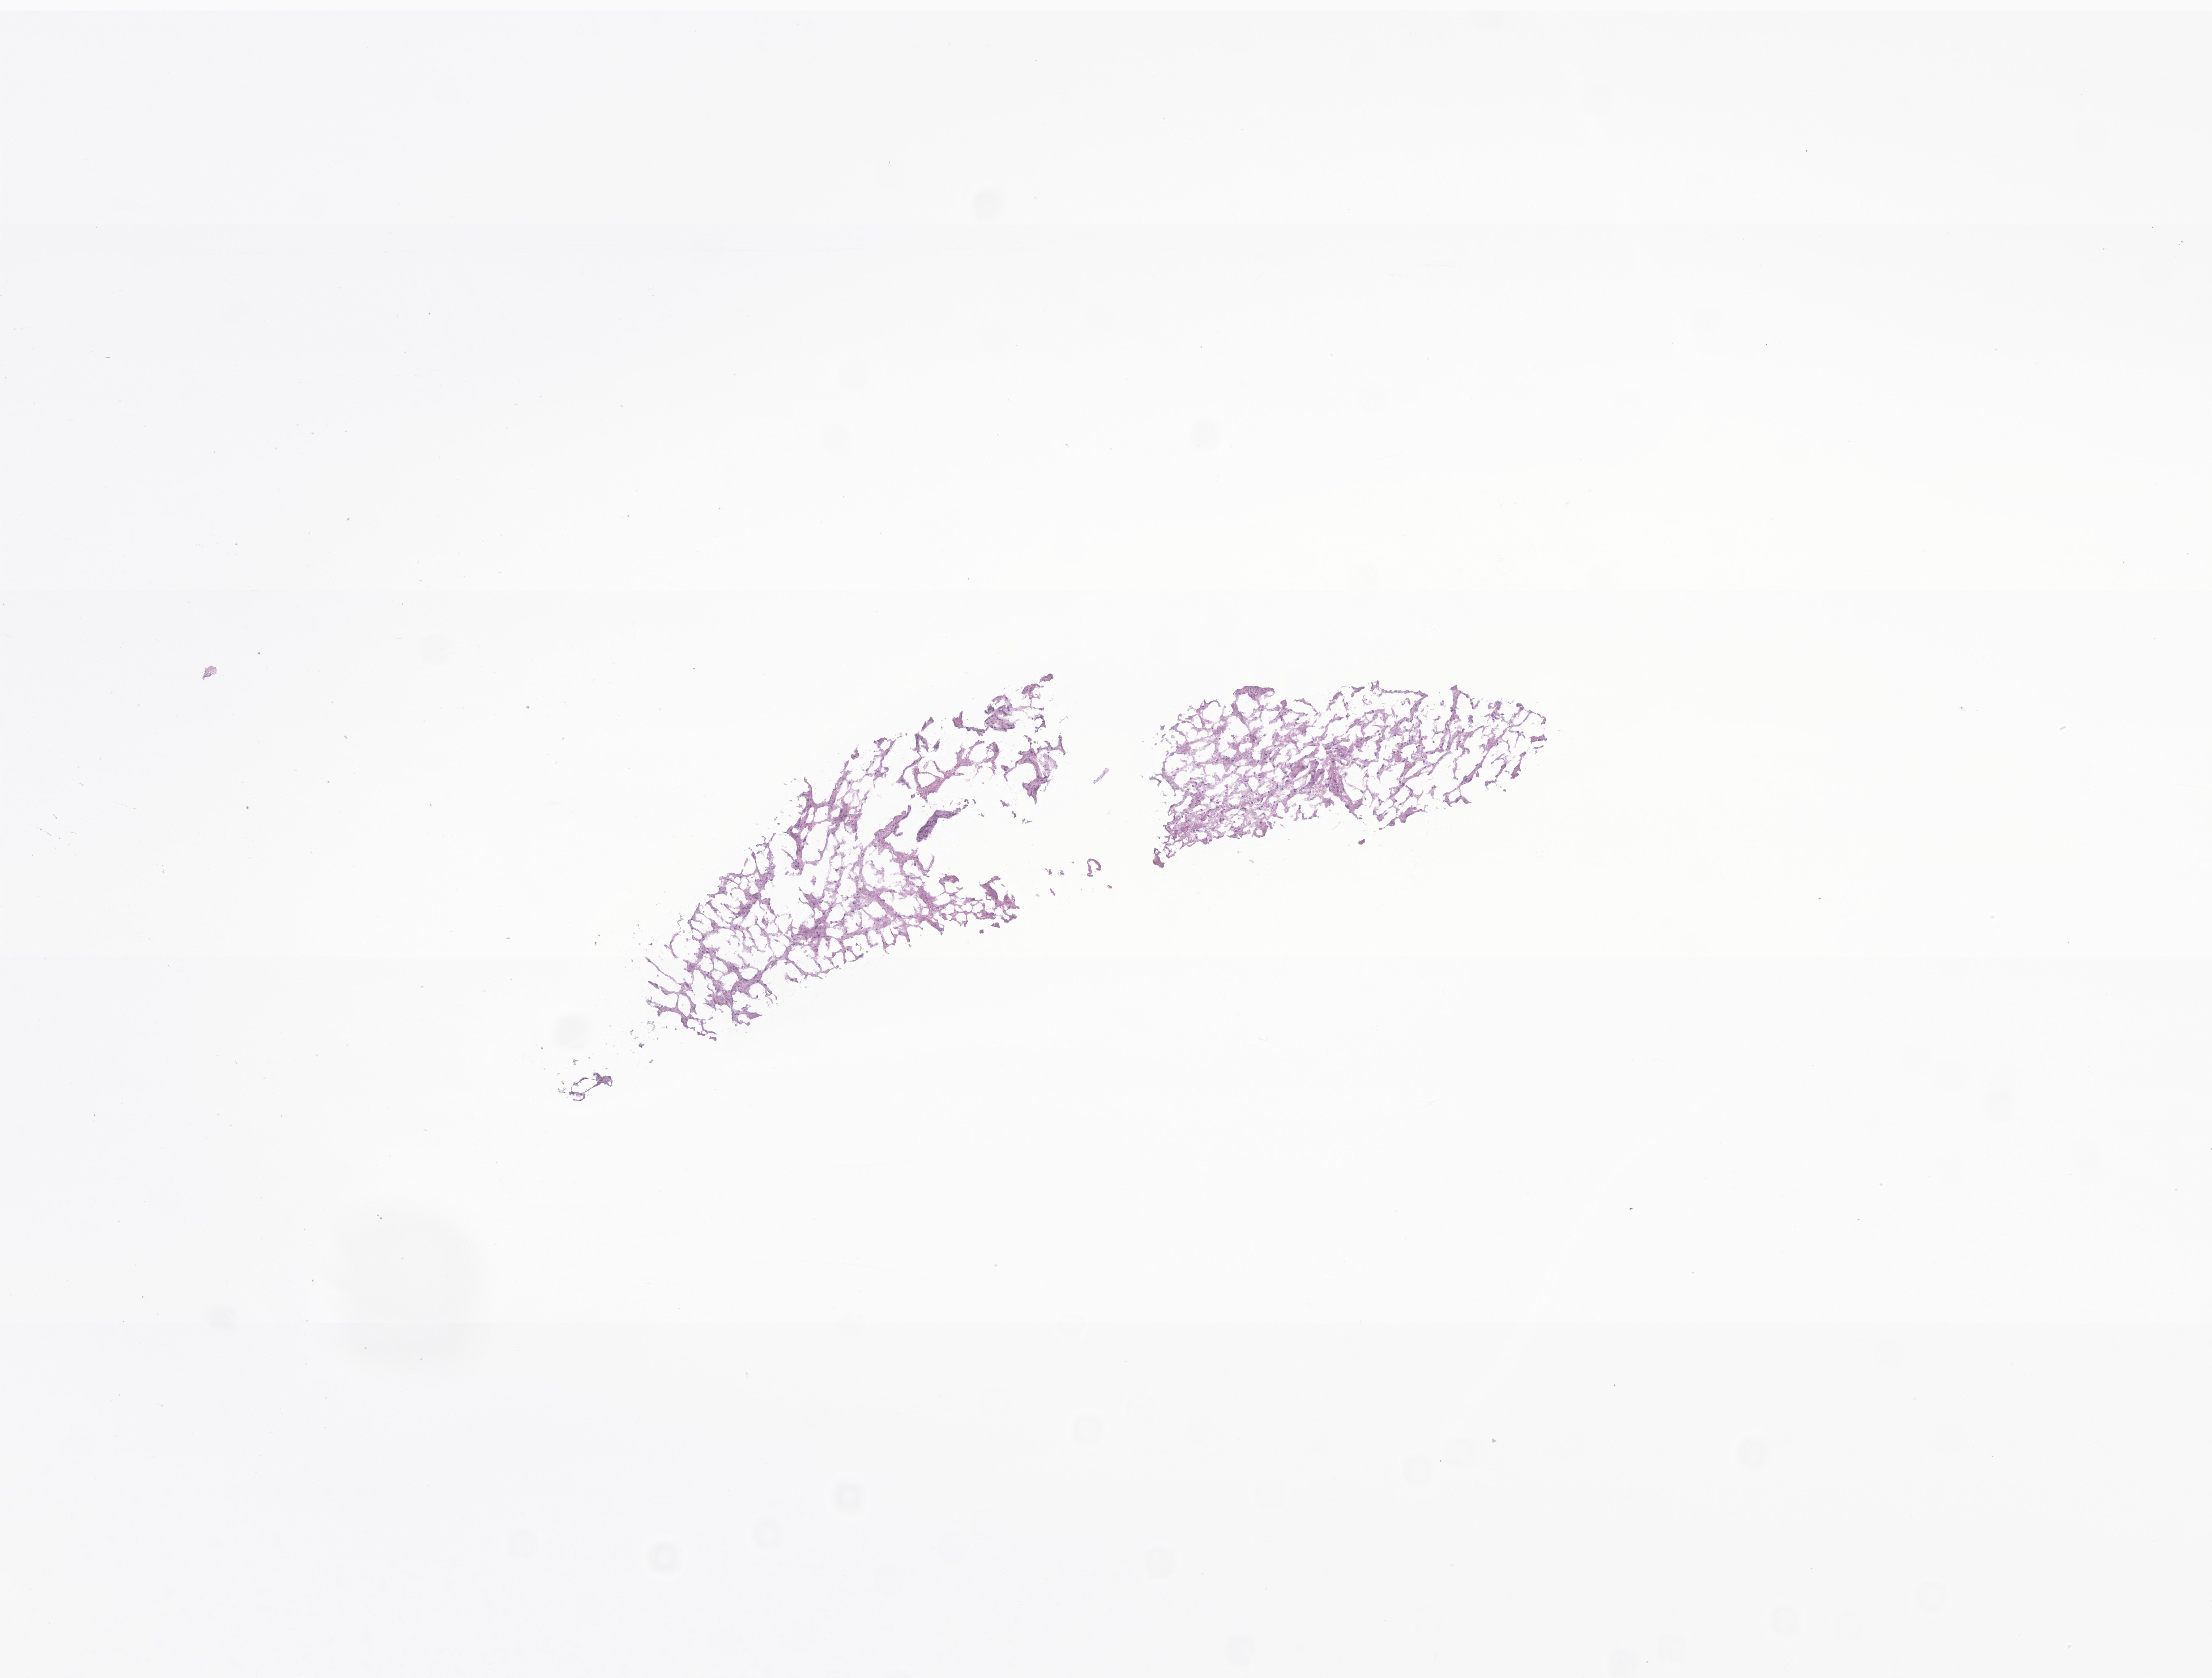
H&E whole-slide image of tumor tissue from the brain, whole scanned area (about 6.4 x 4.9 mm) shown as a low-resolution overview; frozen section. Patient: male, age 181 months (15 years 1 month).
* diagnosis (ICD-O-3 morphology term): Pilocytic astrocytoma